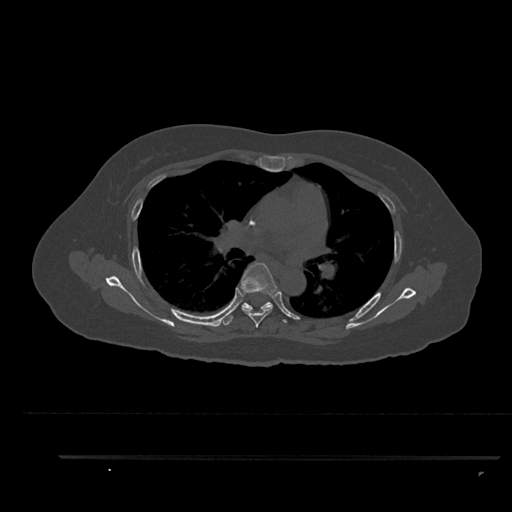
CT including the spine, one axial slice; position 584 of 797 along the scan axis; reconstruction kernel Br40s/3; 120 kVp; bone window (W 1800 / L 400 HU); 0.5 mm slice thickness; 512 × 512 image matrix, field of view 408 × 408 mm. Patient: female, 44 years. Case-level facts recorded for this patient, not image findings: primary cancer: renal.
Annotated regions visible in this slice (semi-automatically segmented with operator editing):
- T5 vertebra: bounding box <240,262,277,328> (left, top, right, bottom; pixels)
- T6 vertebra: <223,302,287,326>